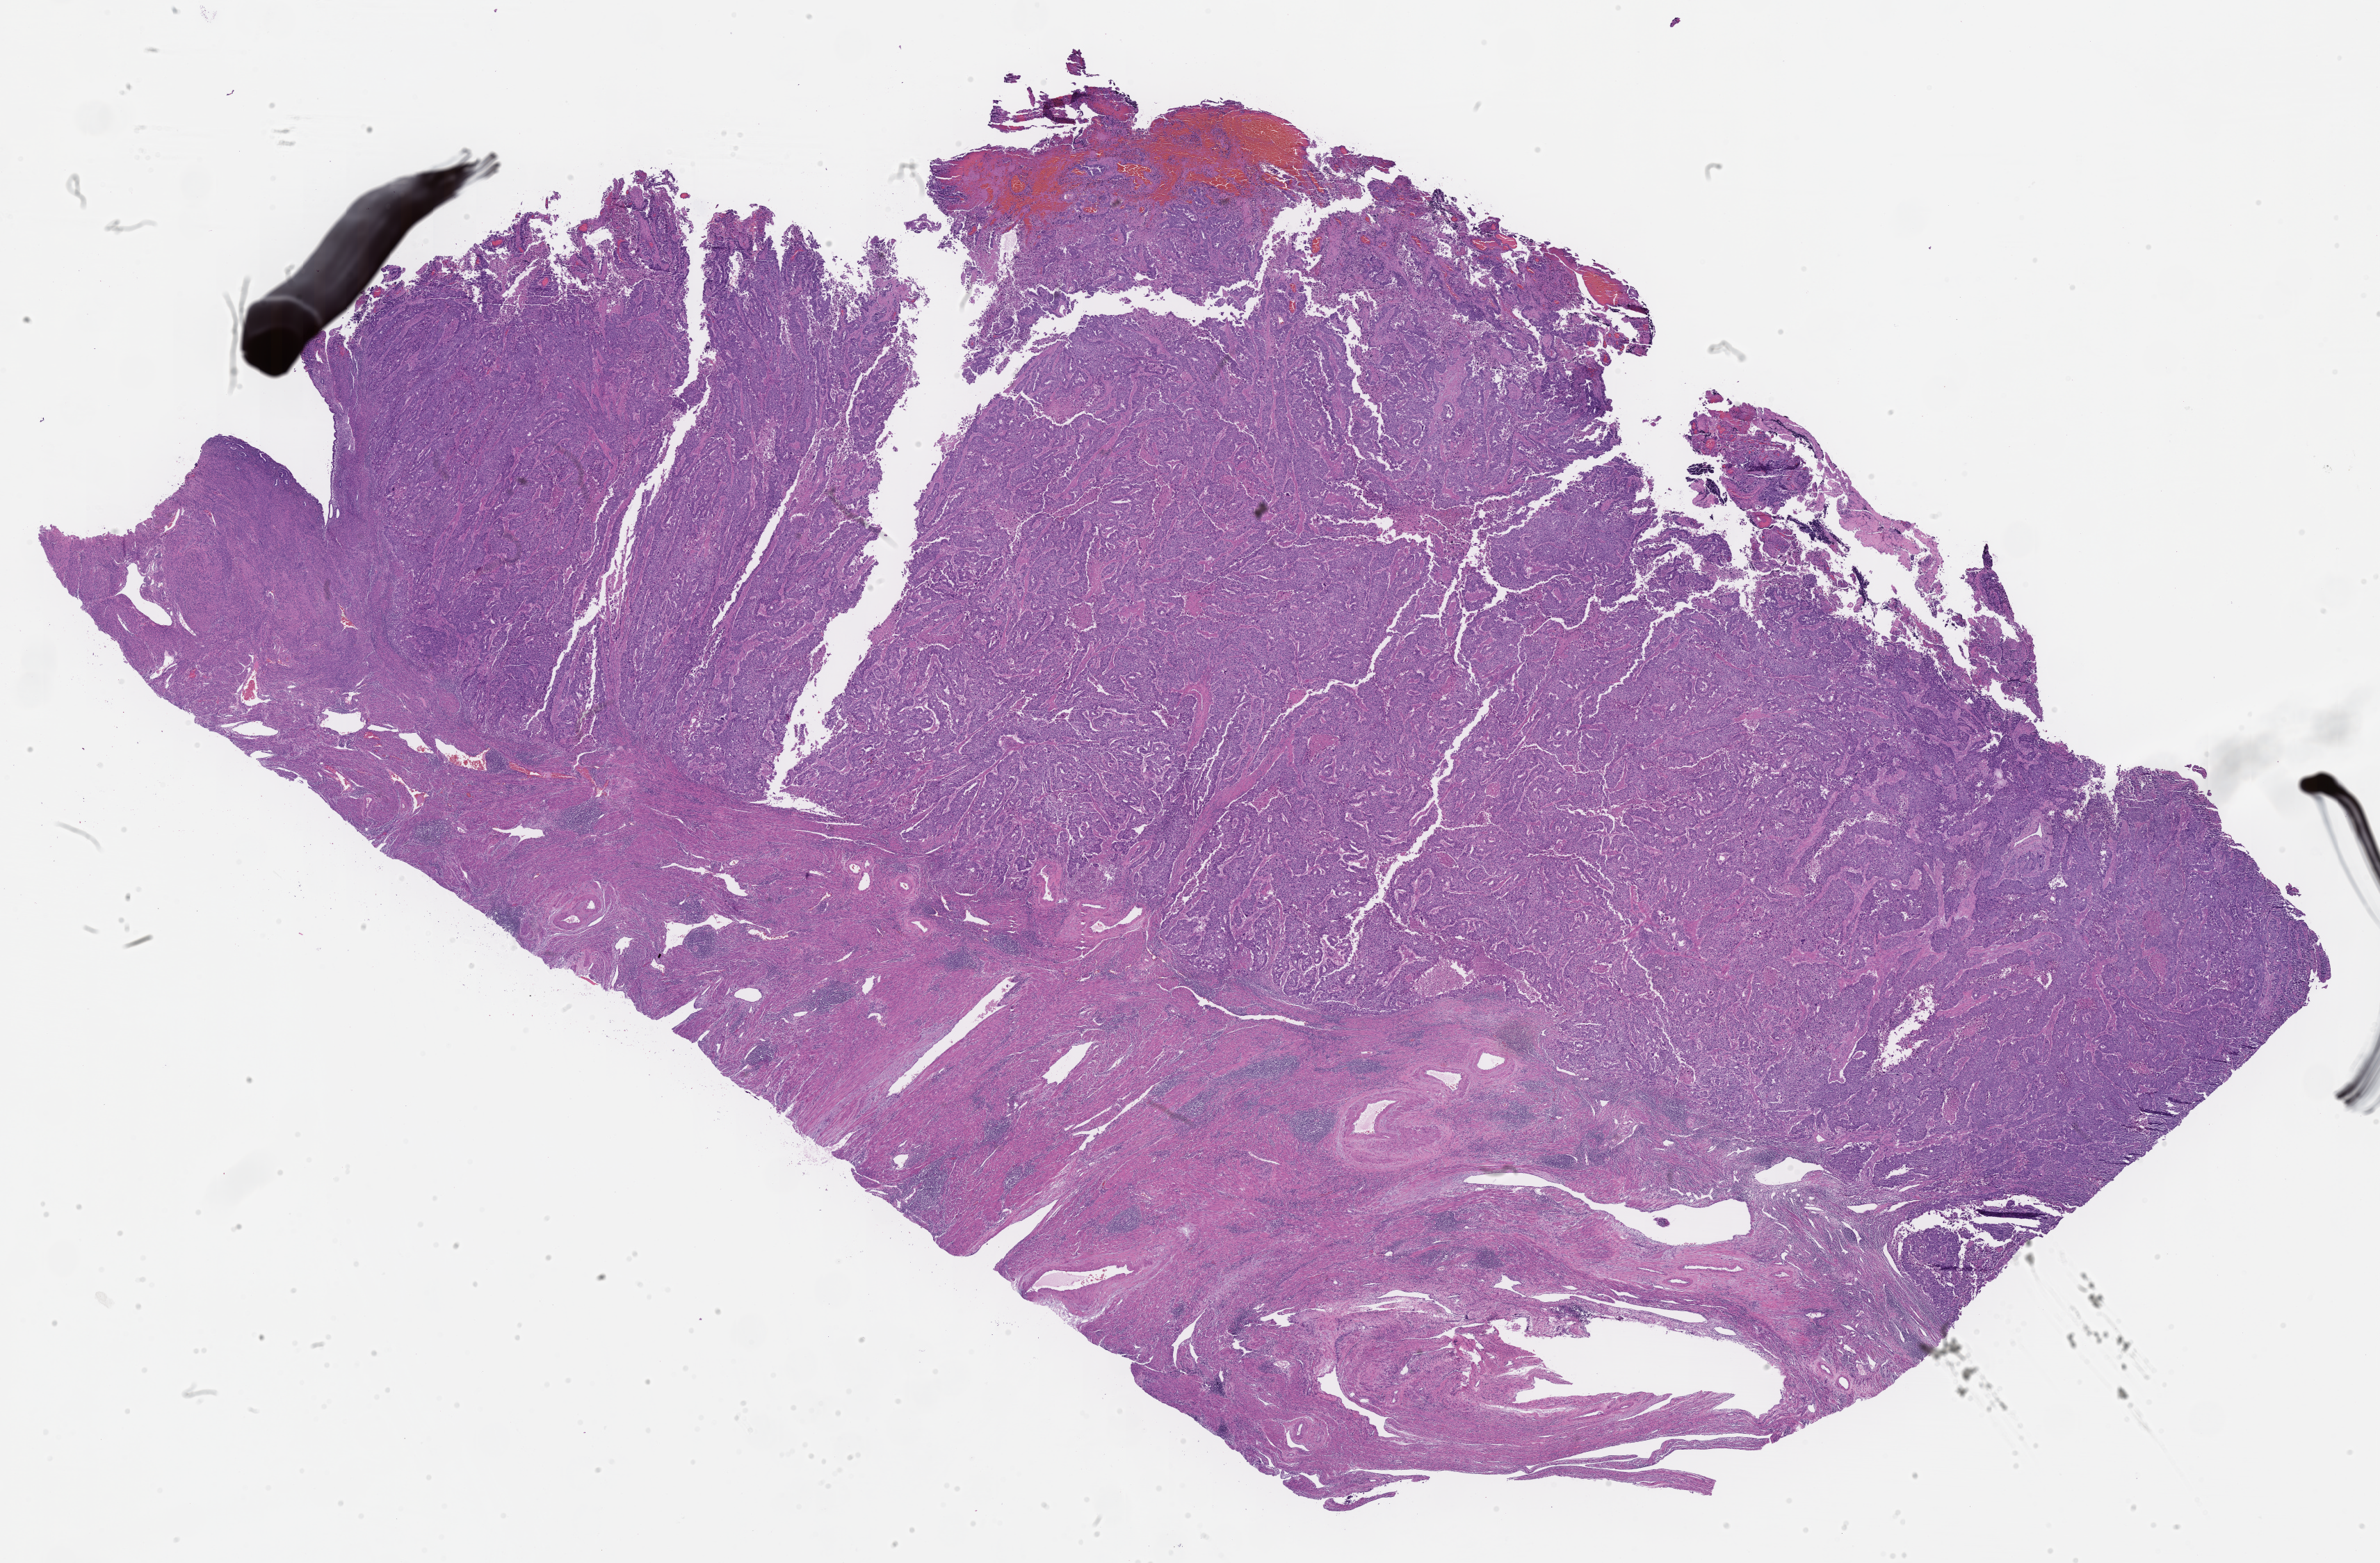
Digitized hematoxylin and eosin (H&E)-stained section, low-resolution overview of the scanned area, about 27.6 x 18.1 mm, FFPE section, primary tumor, site: endometrium. Female, age 54 years at initial diagnosis. Tumor grade: G3 (poorly differentiated). Slide review estimates, as recorded: tumor cells 71%, tumor nuclei 75%, stromal cells 25%, necrosis 4%, normal cells 0%. Infiltration values recorded for this section: lymphocyte infiltration 22%, monocyte infiltration 1%, neutrophil infiltration 0%.
- AJCC pathologic stage: Stage IA
- histologic diagnosis: Endometrioid adenocarcinoma, secretory variant
- section: top of the tissue portion